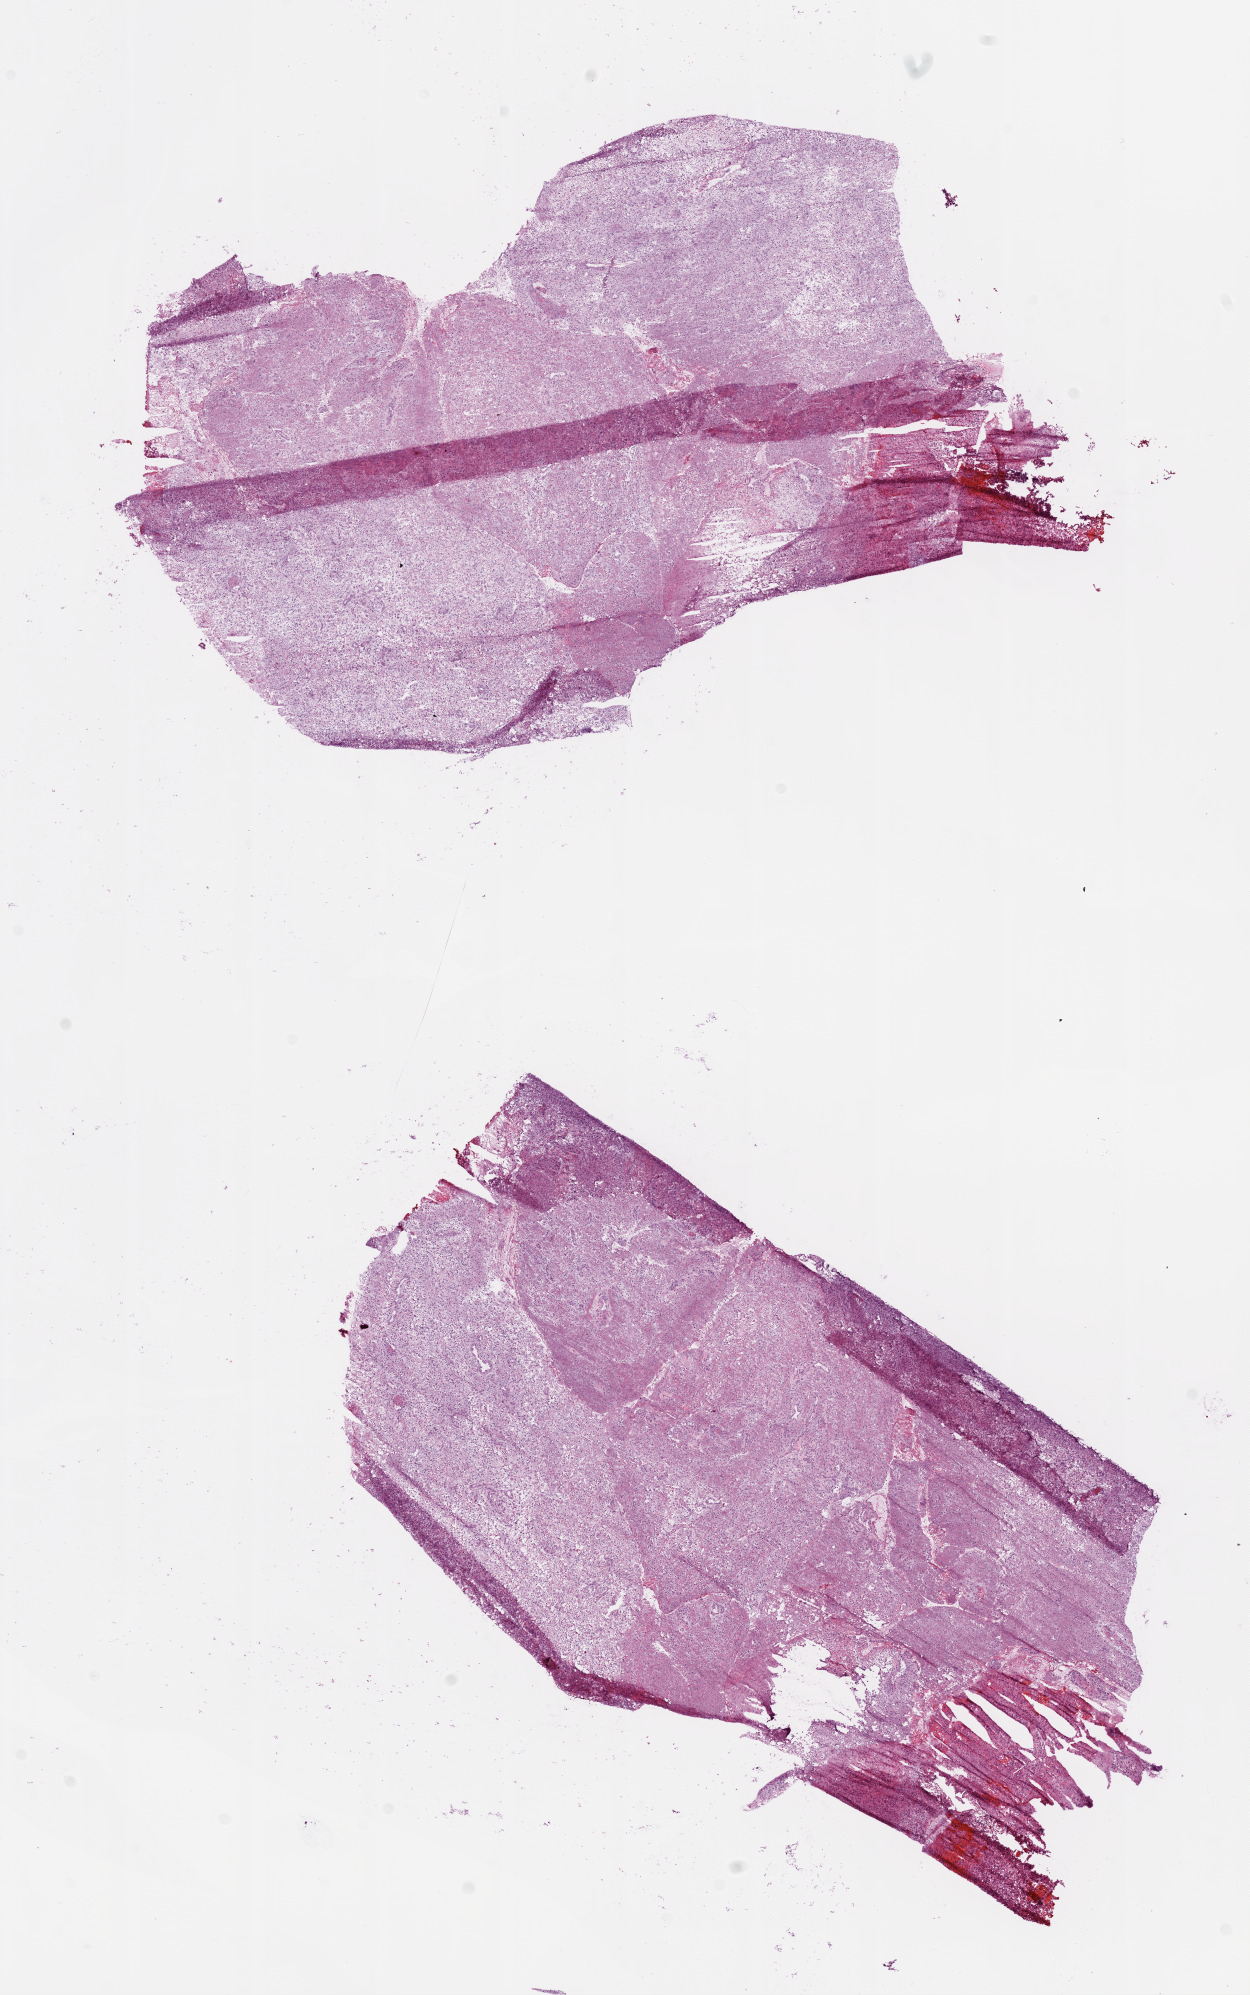
Digitized H&E tissue section (whole slide) — low-resolution overview of the scanned area, about 10.0 x 16.0 mm (acquisition: 20x scan); frozen section from the bottom of the tissue portion; sample: primary tumour, brain. Patient: female, age at initial diagnosis 58 years. Pathologist review of this section (percent, as recorded): tumour cells 80%, tumour nuclei 90%, normal cells 5%, stromal cells 5%, necrosis 10%.
* diagnosis: Glioblastoma